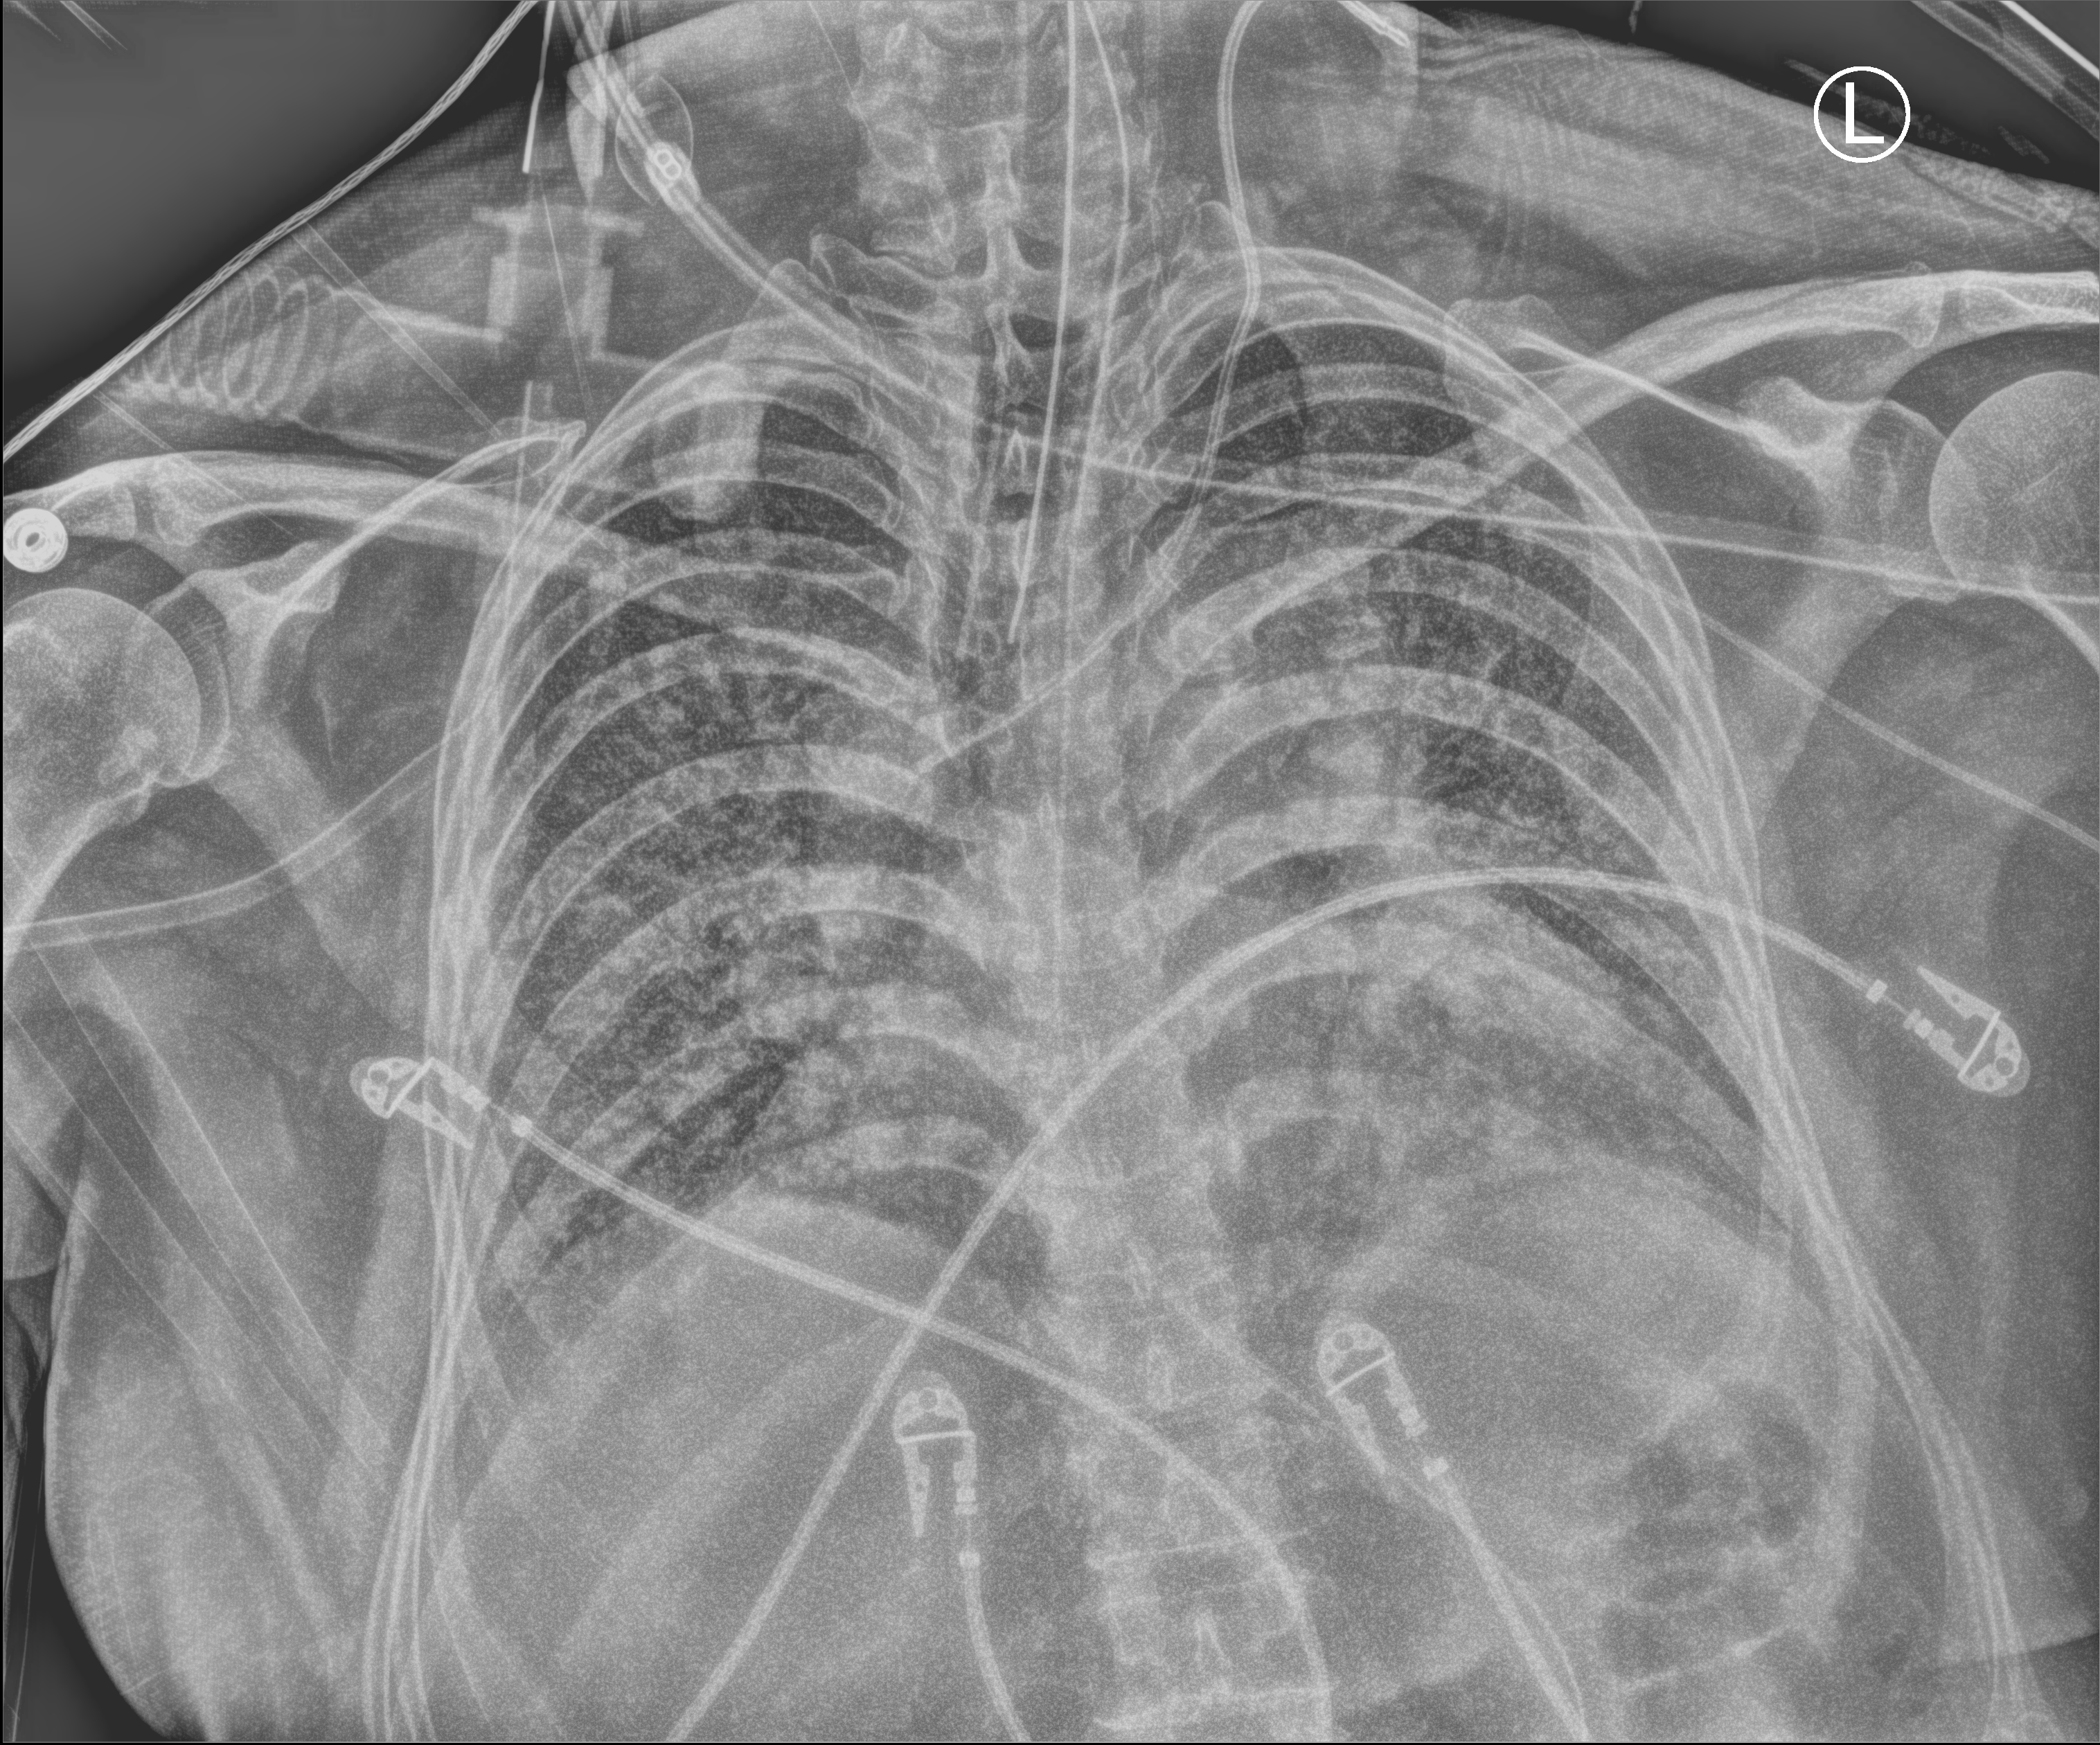
Portable chest radiograph; anteroposterior (AP) projection. Patient hospitalised with COVID-19, aged 18–59 years.
Admission-level facts for this patient (not findings on this image; timing relative to this image not recorded): admitted to intensive care during this hospital stay: yes.